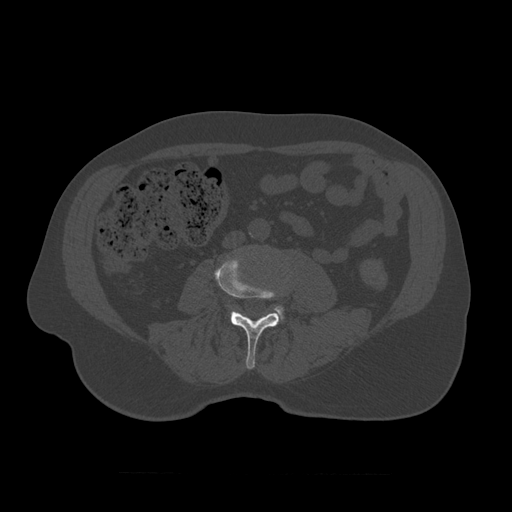
CT including the spine, one axial slice; bone window (W 1800 / L 400 HU); 1.25 mm slice thickness; 512 × 512 image matrix, field of view 405 × 405 mm. Patient age 75 years. From the clinical record (not read from this slice): primary cancer: prostate.
Outlined on this slice (semi-automatically segmented with operator editing):
- L3 vertebra: bounding box (x1, y1, x2, y2) in pixels: (215, 254, 284, 370)
- L4 vertebra: (233, 280, 284, 319)